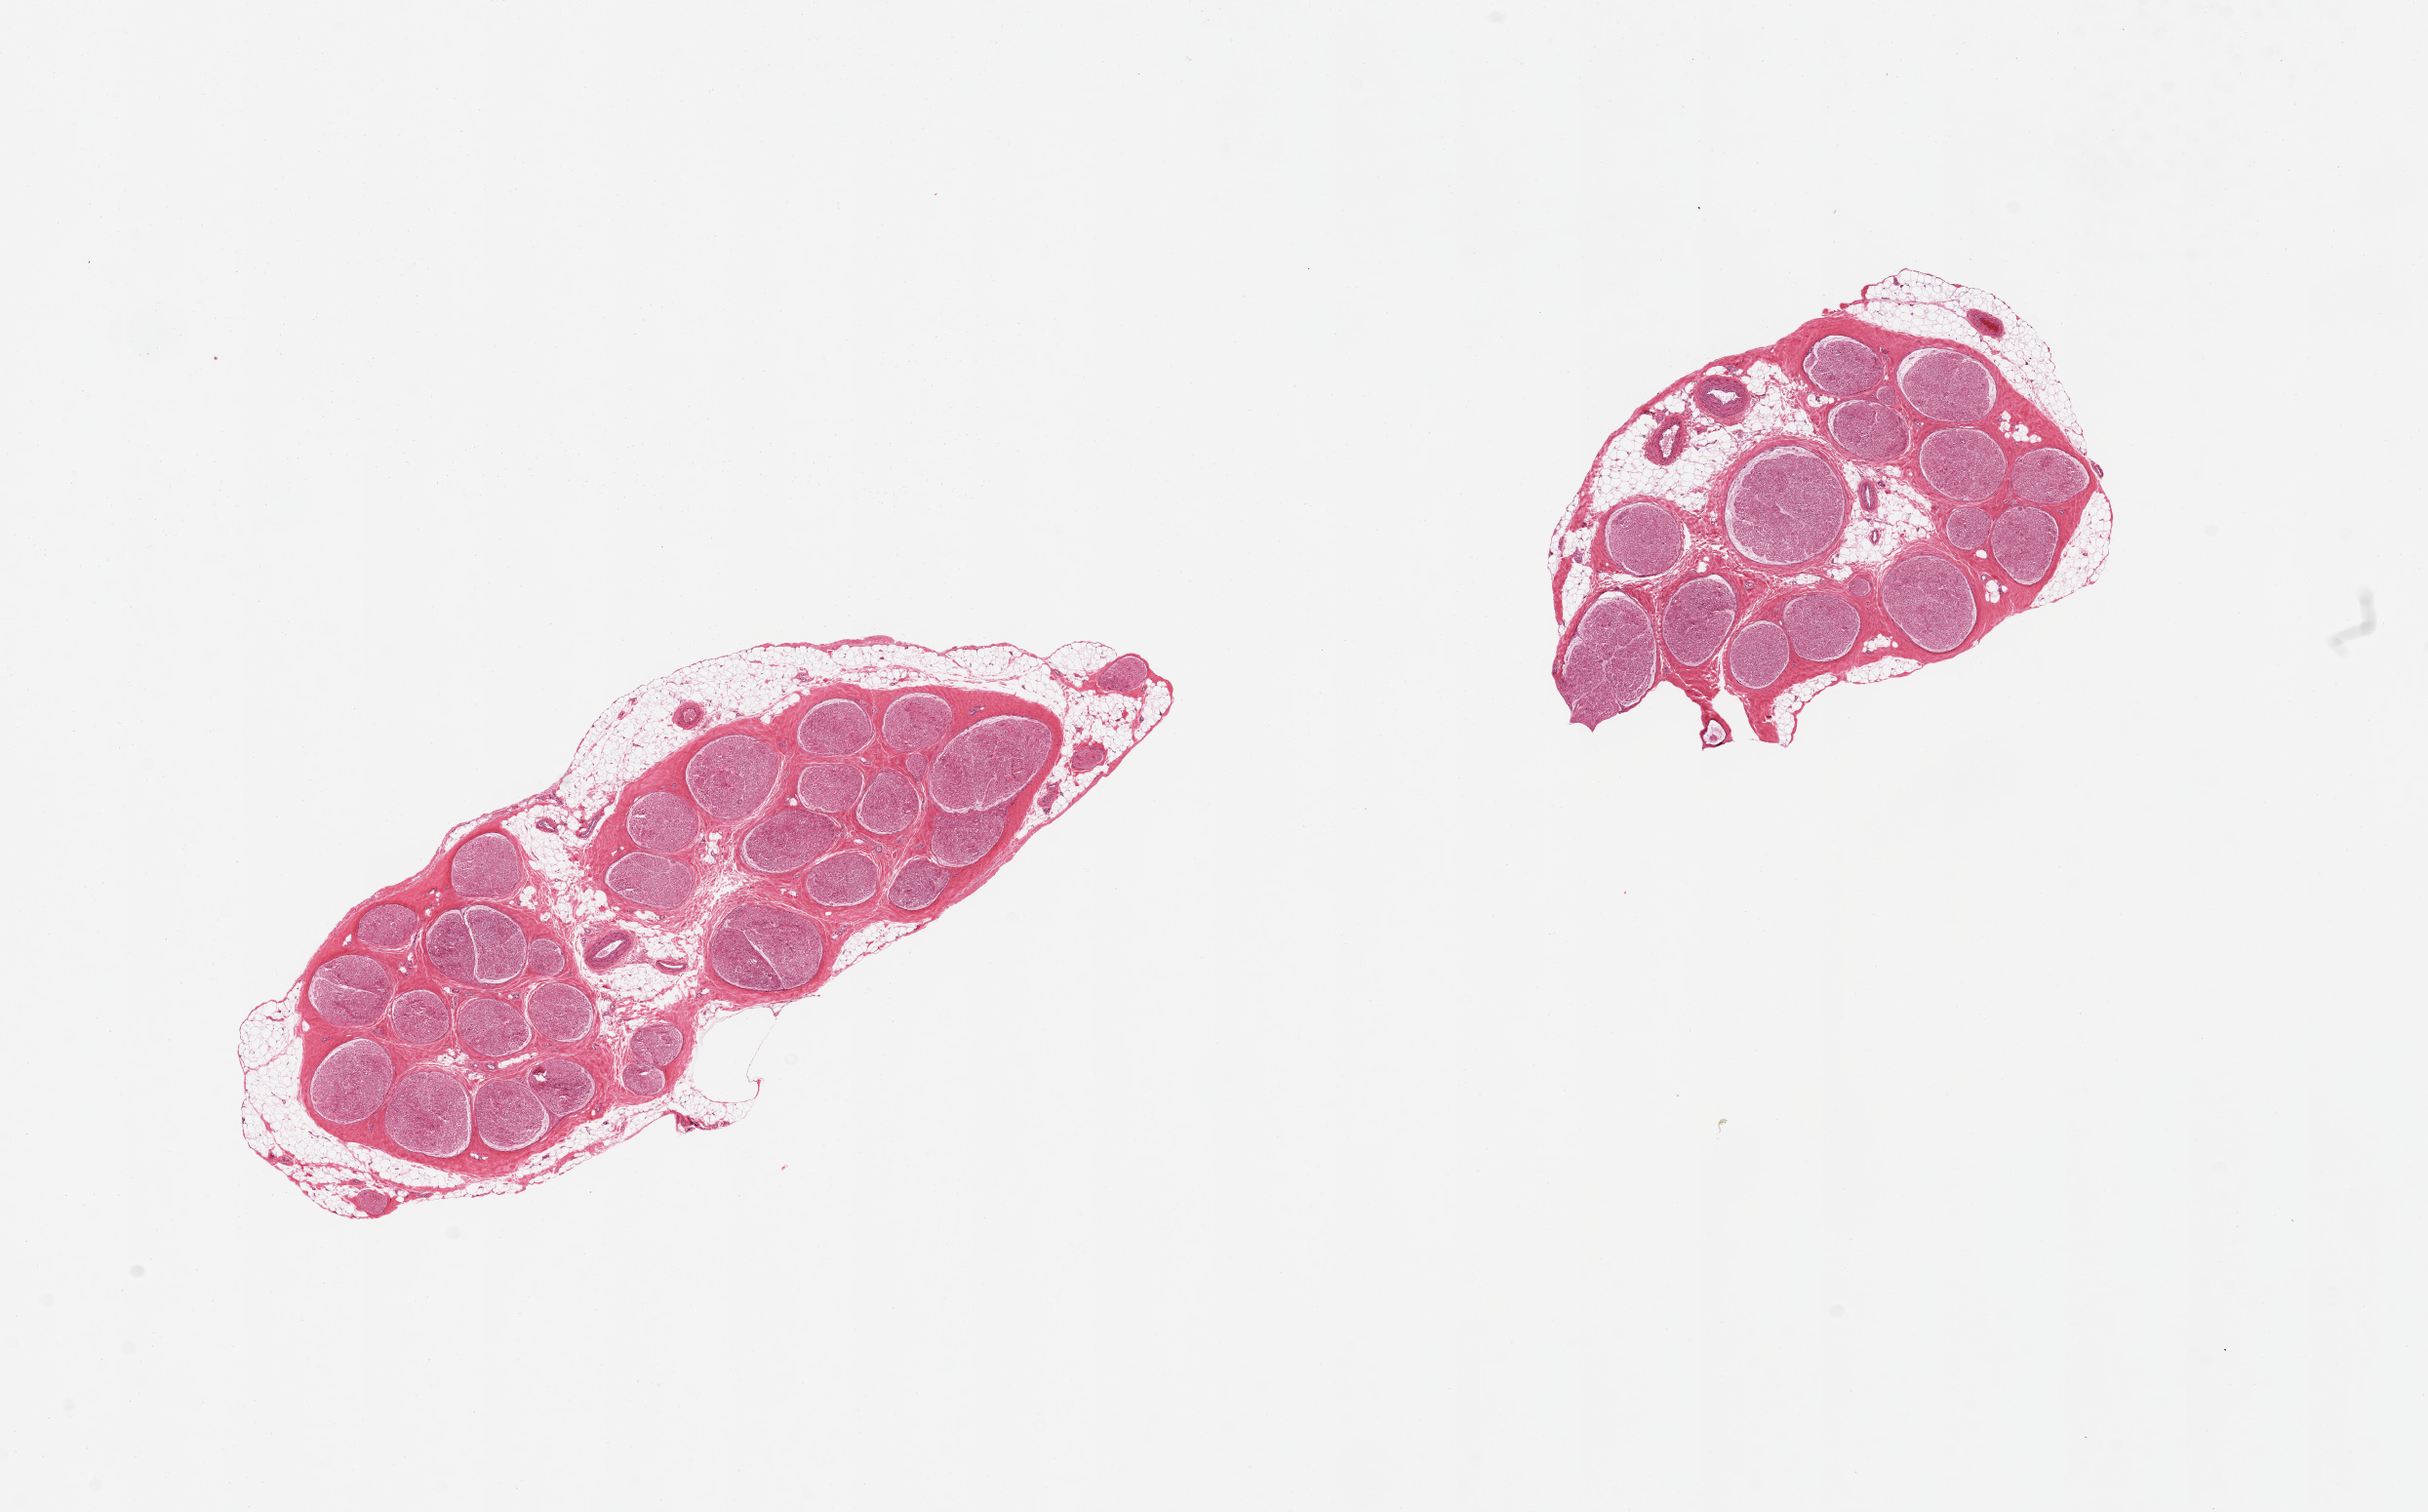
Whole-slide image, H&E stain, a low-resolution overview of the entire scanned area, about 19.7 x 12.3 mm (from a 20x scan); PAXgene-fixed, paraffin-embedded tissue; target tissue: tibial nerve; donor tissue sample. Donor: male.
Review note (as recorded): 2 pieces; 20% external and internal fat.